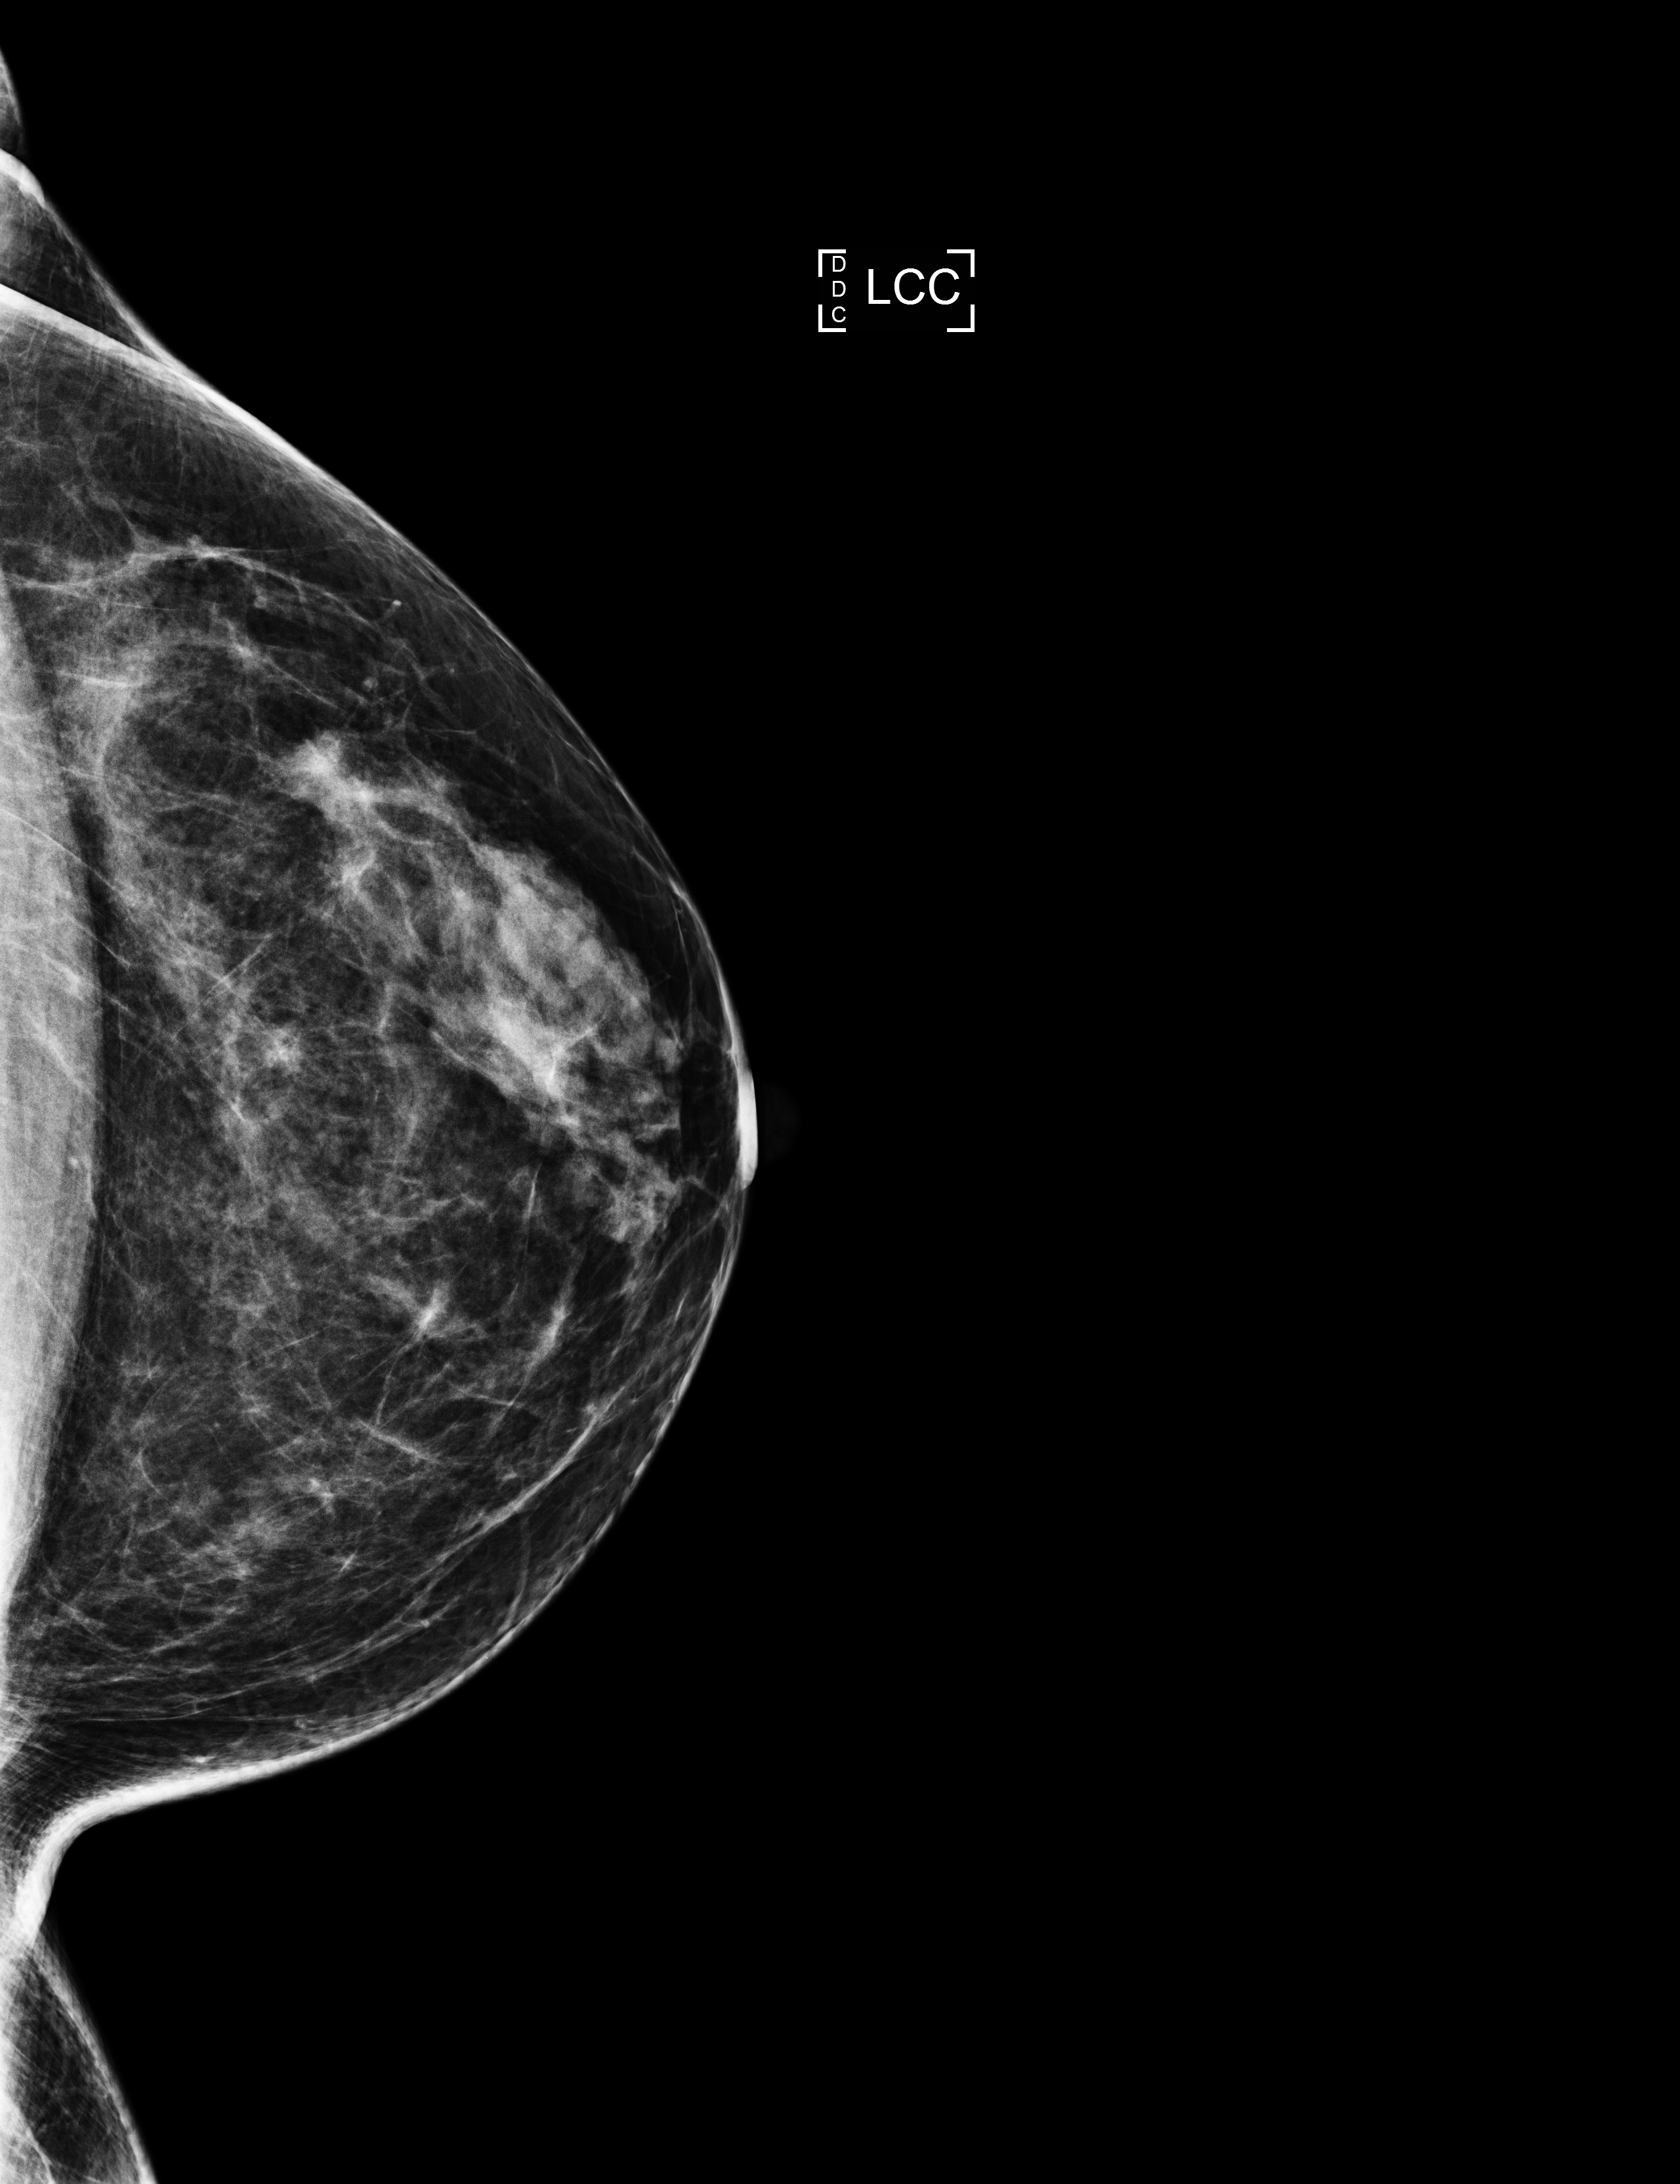
Full-field digital mammogram (FFDM); left breast; cranio-caudal projection; screening examination; compressed breast thickness 64 mm. Patient: female, 59 years.
Breast density at the screening exam (both breasts): heterogeneously dense (BI-RADS density category c). Final BI-RADS assessment for this screening round (tomosynthesis exam, both breasts): category 2. Recall: no recall after this screen.